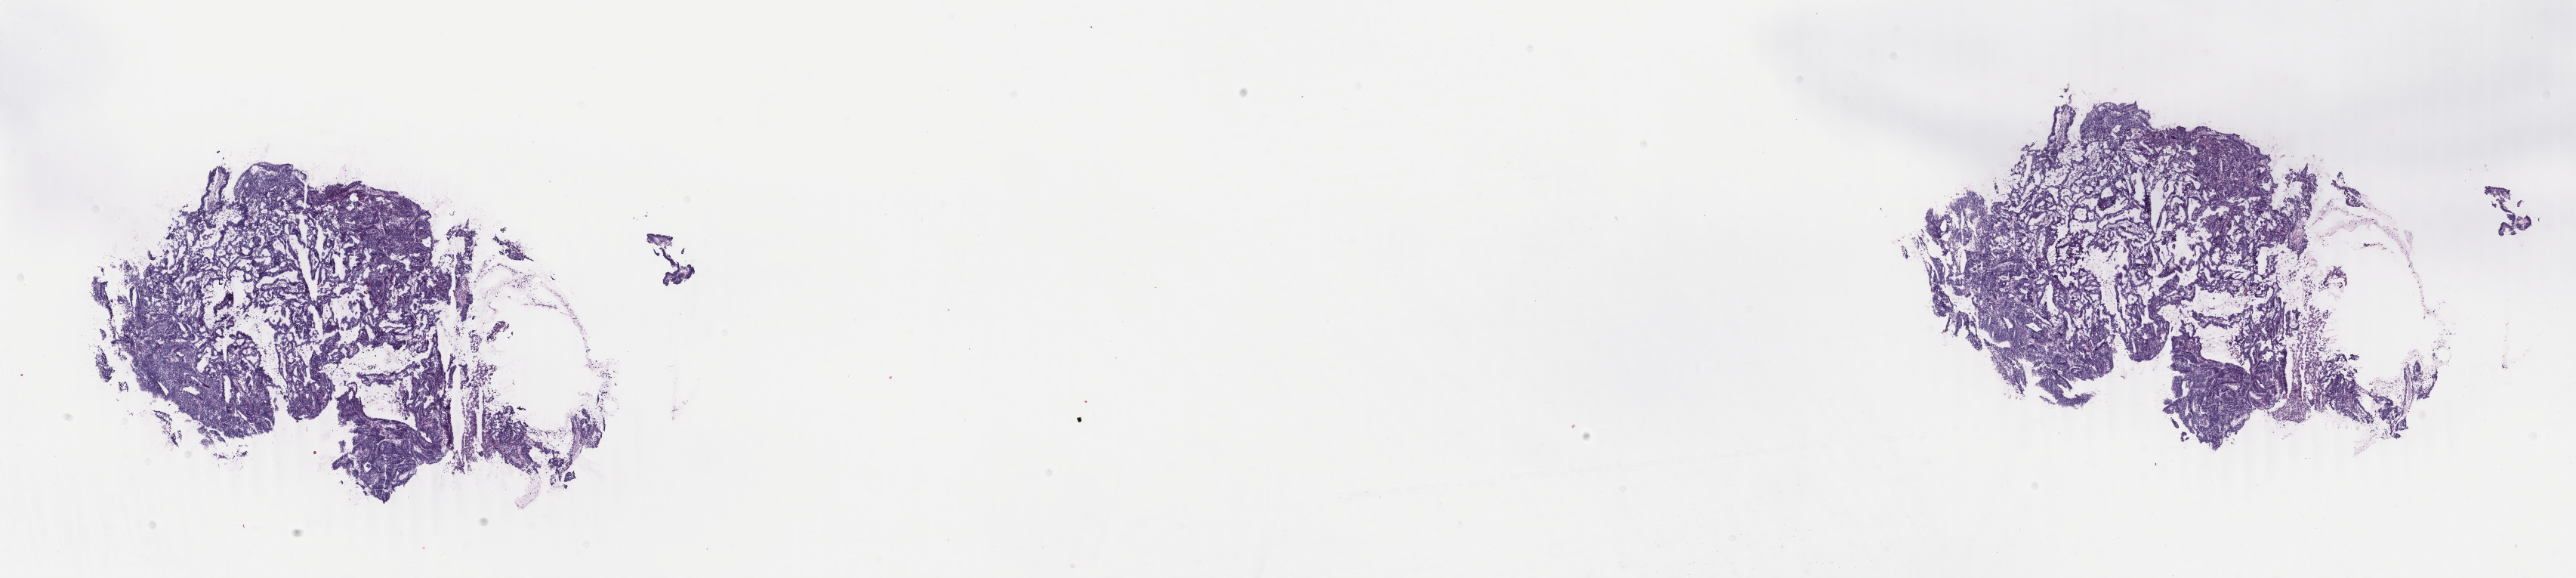
Whole-slide histology image, H&E — shown as a low-resolution overview of the whole scanned area (about 27.1 x 6.1 mm, acquisition: 40x scan), frozen section, uterus, primary tumour sample. Patient: female, age at initial diagnosis 73 years. Histologic grade: G1 (well differentiated). Composition of this section per pathologist review: tumour cells 85%, tumour nuclei 85%, normal cells 0%, stromal cells 5%, necrosis 10%. Inflammatory infiltration, as recorded: lymphocyte infiltration 2%, monocyte infiltration 1%, neutrophil infiltration 7%.
Diagnosis: Endometrioid adenocarcinoma, NOS (endometrium). FIGO stage: IA.